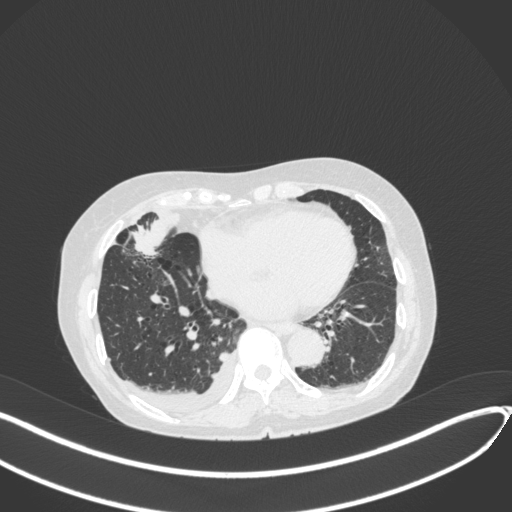
Chest CT, one axial slice; slice 138 of 418 in the series (ordered by position); 120 kVp; lung window (W 1500 / L -600 HU); 512 × 512 image matrix. Female patient, age 75 years. From the clinical record (not read from this slice): clinical TNM (as recorded): T2a N3 M0.
Annotated regions visible in this slice (rectangle marked by the reading radiologist):
- lung tumour (recorded histology: adenocarcinoma): bounding box <127,211,185,255> (left, top, right, bottom; pixels)